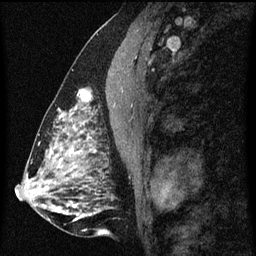
Breast MRI (dynamic contrast-enhanced), one sagittal slice; dynamic contrast-enhanced series, image 2 of 3 at this slice position (ordered by acquisition); 1.5 T; TE 4.2 ms, TR 8 ms; 256 × 256 image matrix, field of view 180 × 180 mm. Female patient, age 51 years.
Outlined on this slice (semi-automatically segmented with operator editing):
- analysis volume of interest (the breast-tissue region the enhancement analysis was run in; not a lesion): bounding box [x1, y1, x2, y2] px = [61, 70, 100, 129]
- tumour enhancement mask (voxels above the 70 % enhancement threshold inside the analysis volume of interest): [61, 90, 93, 129]